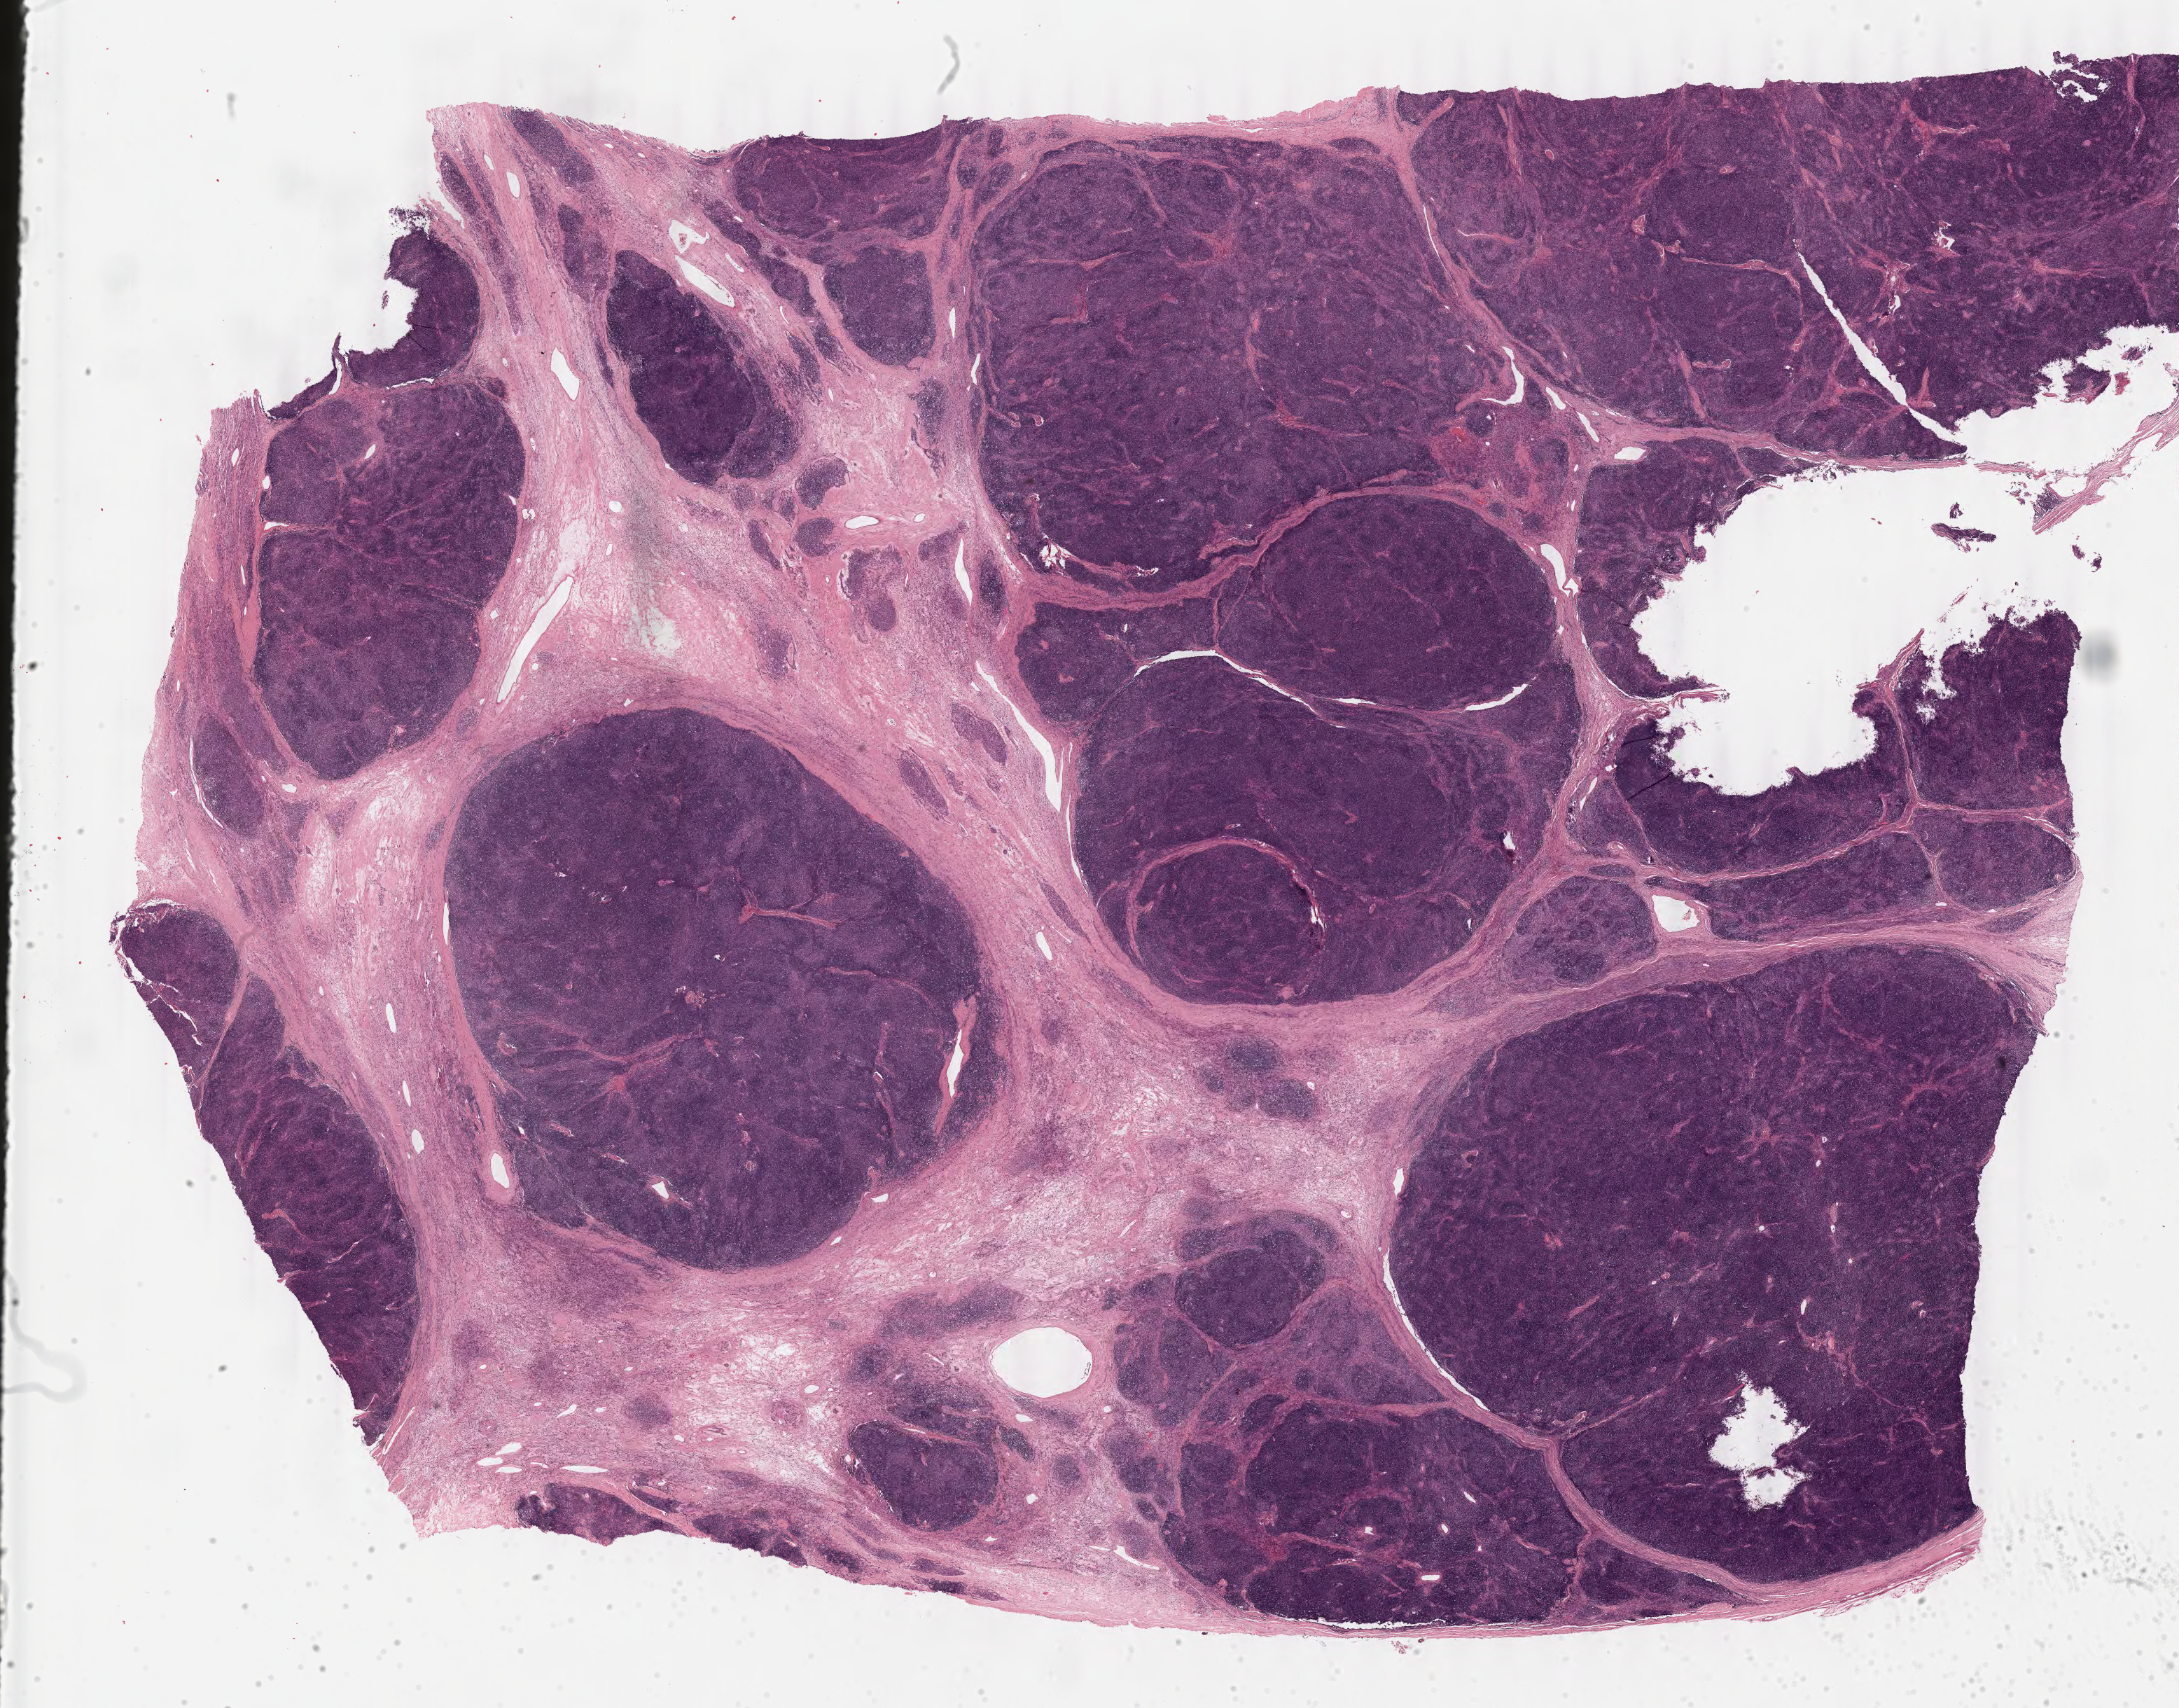
Whole-slide histology image, H&E-stained — low-resolution overview of the scanned area, about 24.6 x 19.3 mm (acquisition: 40x scan), formalin-fixed paraffin-embedded (FFPE) diagnostic section, thymus, primary tumour sample. Patient: female, age at initial diagnosis 61 years.
Diagnosis: Thymoma, type AB, malignant.